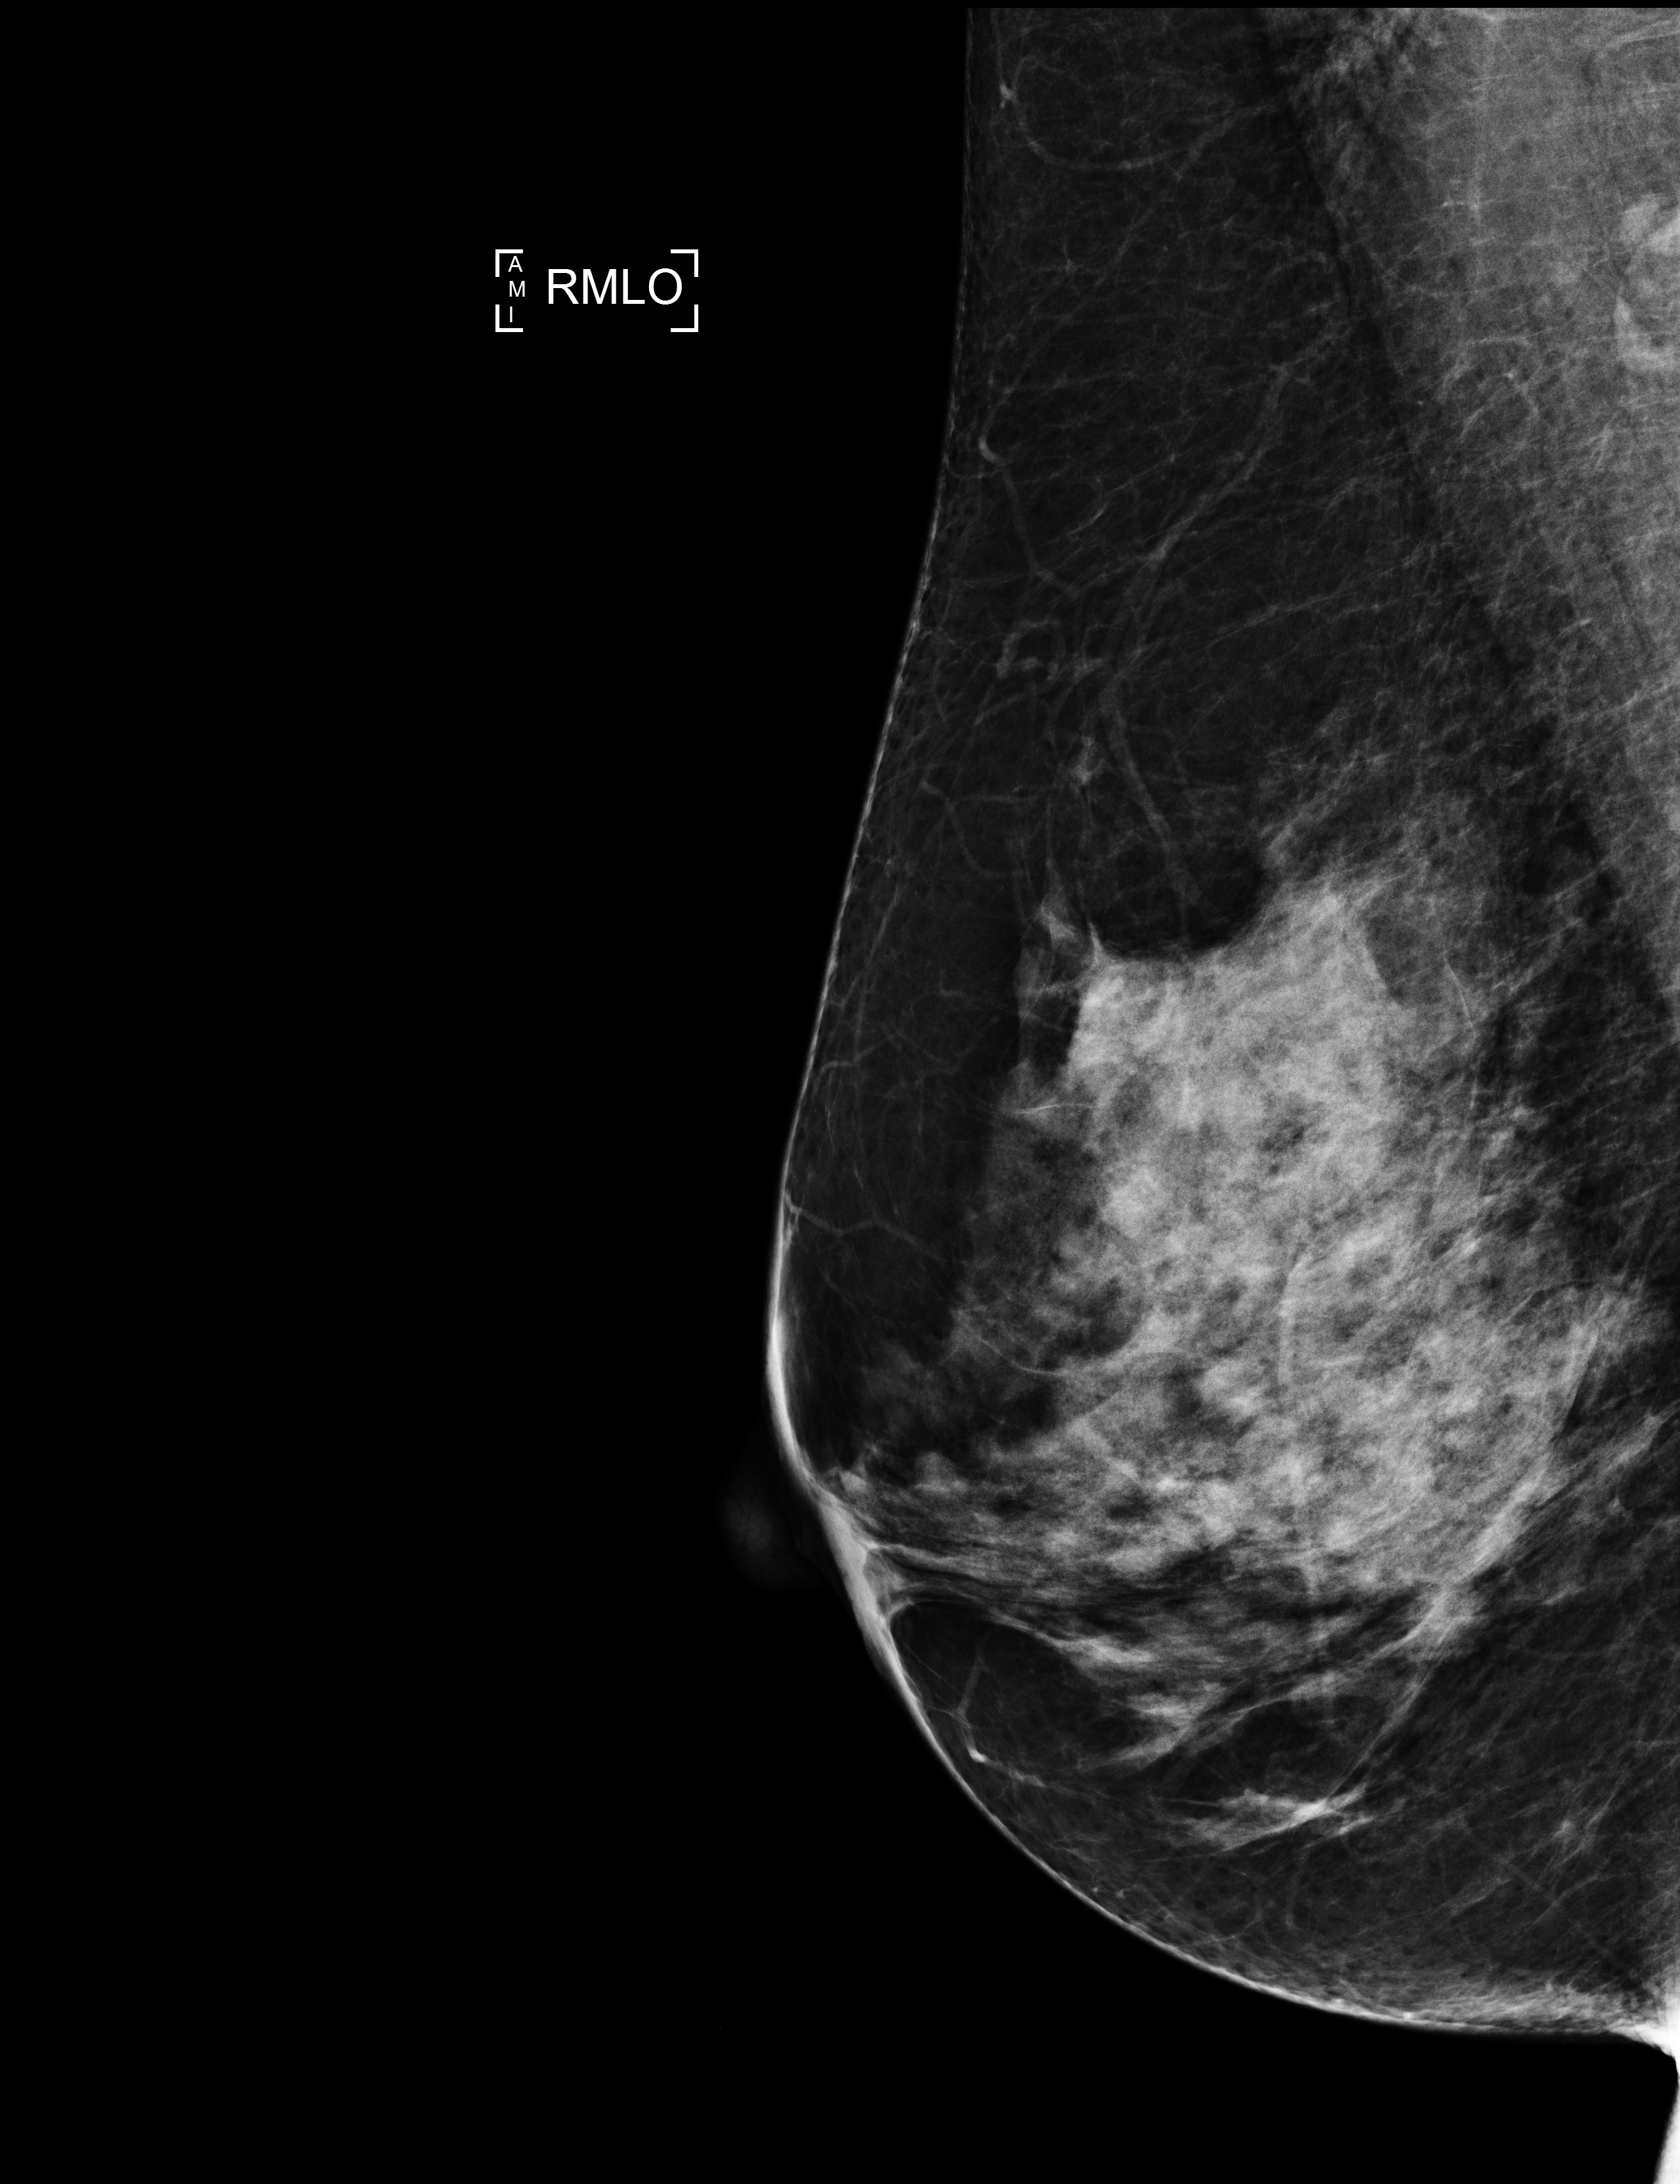
Annual screening mammography examination; compressed breast thickness 68 mm.
Image type: full-field digital mammogram. Breast: right. Projection: MLO view.